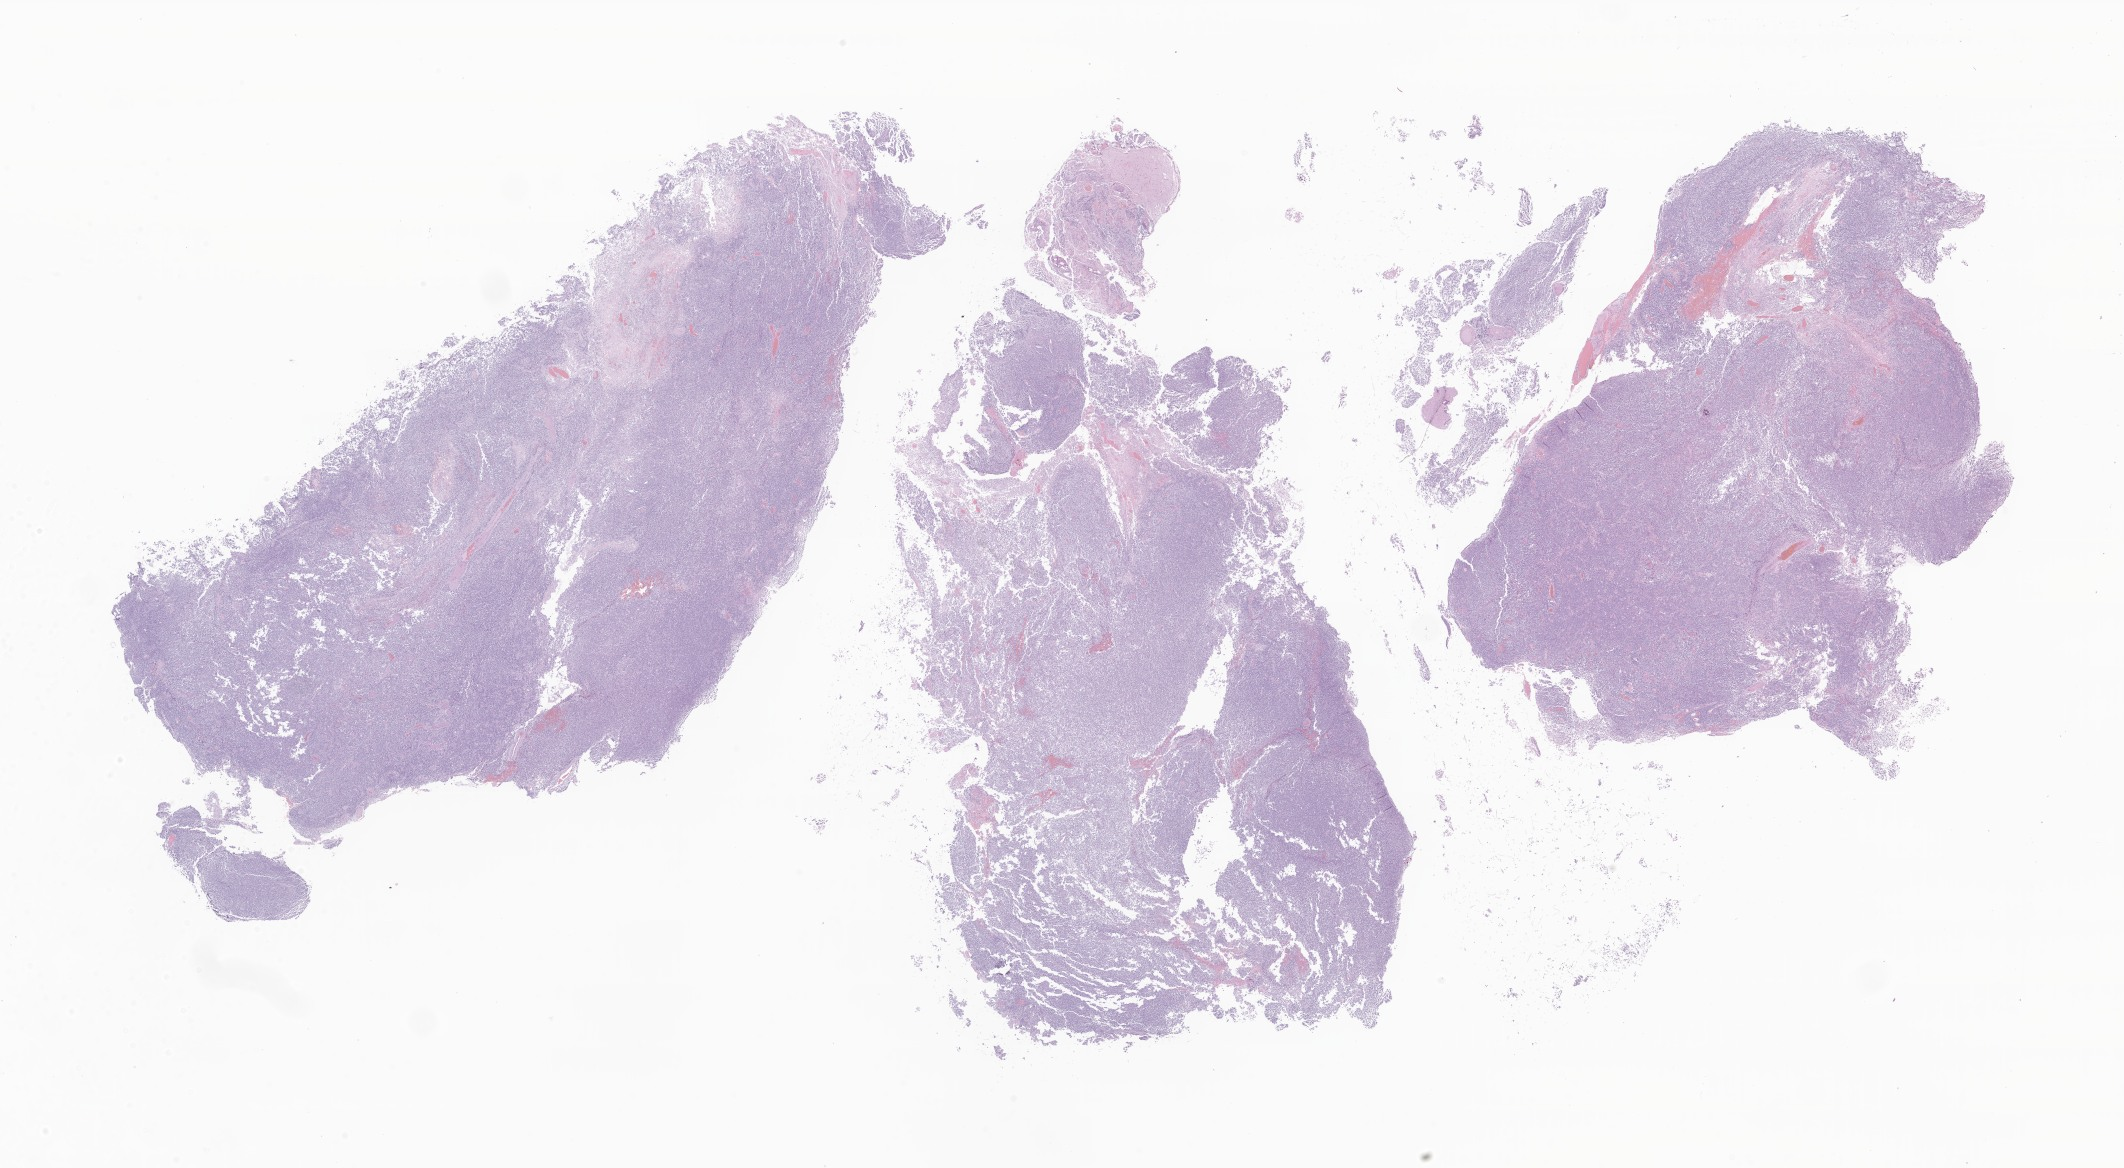
Haematoxylin and eosin whole-slide image of tumor tissue from the cerebral ventricle, whole scanned area (about 35.8 x 19.7 mm) shown as a low-resolution overview; formalin-fixed paraffin-embedded section. Patient: female, age 82 months (6 years 10 months).
- recorded diagnosis: Glioma, malignant